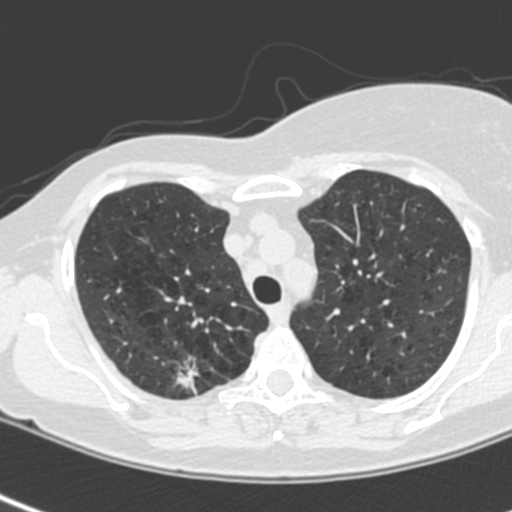
Low-dose screening chest CT, one axial slice; slice 173 of 214 in the series (ordered by position); 120 kVp; lung window (W 1500 / L -600 HU); 1.3 mm slice thickness; 512 × 512 image matrix, field of view 281 × 281 mm.
Structures marked on this image (expert manual segmentation):
- lesion 1 (tumor, upper lobe of right lung): bounding box [x1, y1, x2, y2] px = [176, 363, 197, 393]